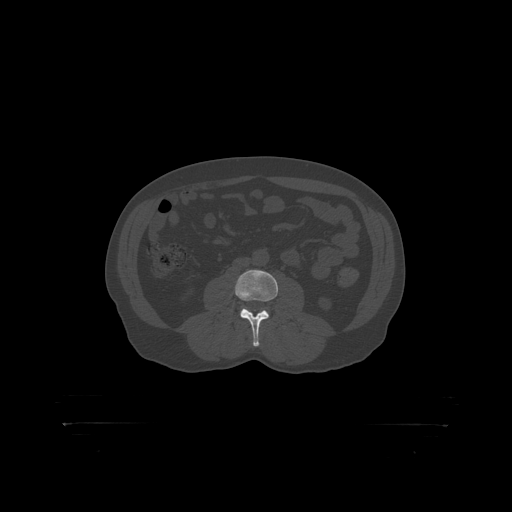
CT including the spine, one axial slice. Position 259 of 399 along the scan axis. Reconstruction kernel STANDARD. Bone window (W 1800 / L 400 HU). 512 × 512 image matrix, field of view 650 × 650 mm. Male patient, age 46 years. Case-level facts recorded for this patient, not image findings: primary cancer: skin.
Annotated regions visible in this slice (semi-automatically segmented with operator editing):
- L3 vertebra: bounding box [x1, y1, x2, y2] px = [235, 270, 278, 319]